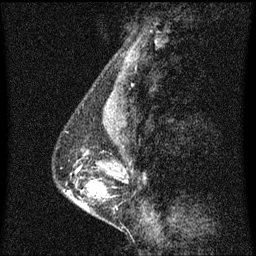
Breast MRI (dynamic contrast-enhanced), one sagittal slice. Position 22 of 60 along the scan axis. Dynamic contrast-enhanced series, image 2 of 3 at this slice position (ordered by acquisition). 1.5 T. TE 4.2 ms, TR 8.4 ms. 256 × 256 image matrix, field of view 200 × 200 mm. Patient: female, 40 years. From the clinical record (not read from this slice): setting: breast cancer imaged before/during neoadjuvant chemotherapy; receptor status: triple-negative.
Annotated regions visible in this slice (semi-automatic segmentation, software-assisted and operator-edited):
- analysis volume of interest (the breast-tissue region the enhancement analysis was run in; not a lesion): box from (x=65, y=128) to (x=120, y=211) px
- tumour enhancement mask (voxels above the 70 % enhancement threshold inside the analysis volume of interest): (x=93, y=188)–(x=106, y=197)